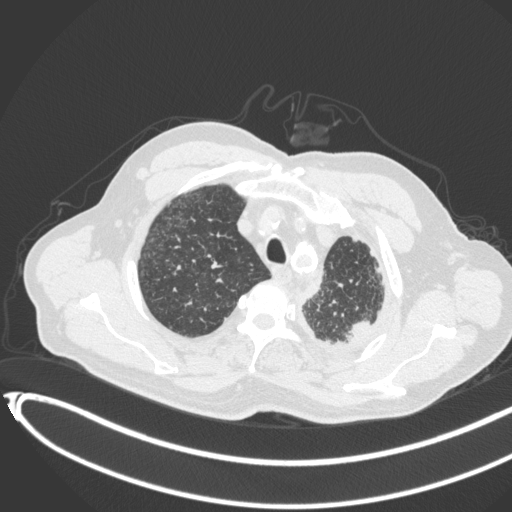
Chest CT, one axial slice. Position 361 of 451 along the scan axis. 120 kVp. Lung window (W 1500 / L -600 HU). 1 mm slice thickness. 512 × 512 image matrix, field of view 400 × 400 mm. Male patient, age 78 years. From the clinical record (not read from this slice): clinical TNM (as recorded): T1c N0 M1.
Annotated regions visible in this slice (bounding box drawn by a radiologist):
- lung tumour (recorded histology: adenocarcinoma): bounding box (x1, y1, x2, y2) in pixels: (344, 318, 372, 343)